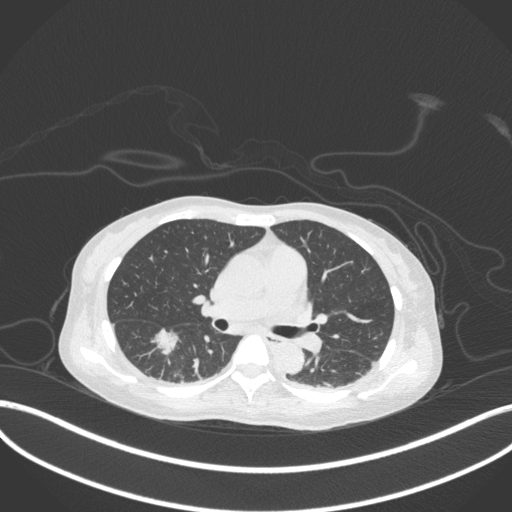
Chest CT, one axial slice; position 176 of 260 along the scan axis; reconstruction kernel B31f; 120 kVp; lung window (W 1500 / L -600 HU); 512 × 512 image matrix, field of view 400 × 400 mm. Patient: female, 44 years. From the clinical record (not read from this slice): clinical TNM (as recorded): T1c N0 M0.
Annotated regions visible in this slice (bounding box drawn by a radiologist):
- lung tumour (recorded histology: adenocarcinoma): bounding box <149,321,182,361> (left, top, right, bottom; pixels)